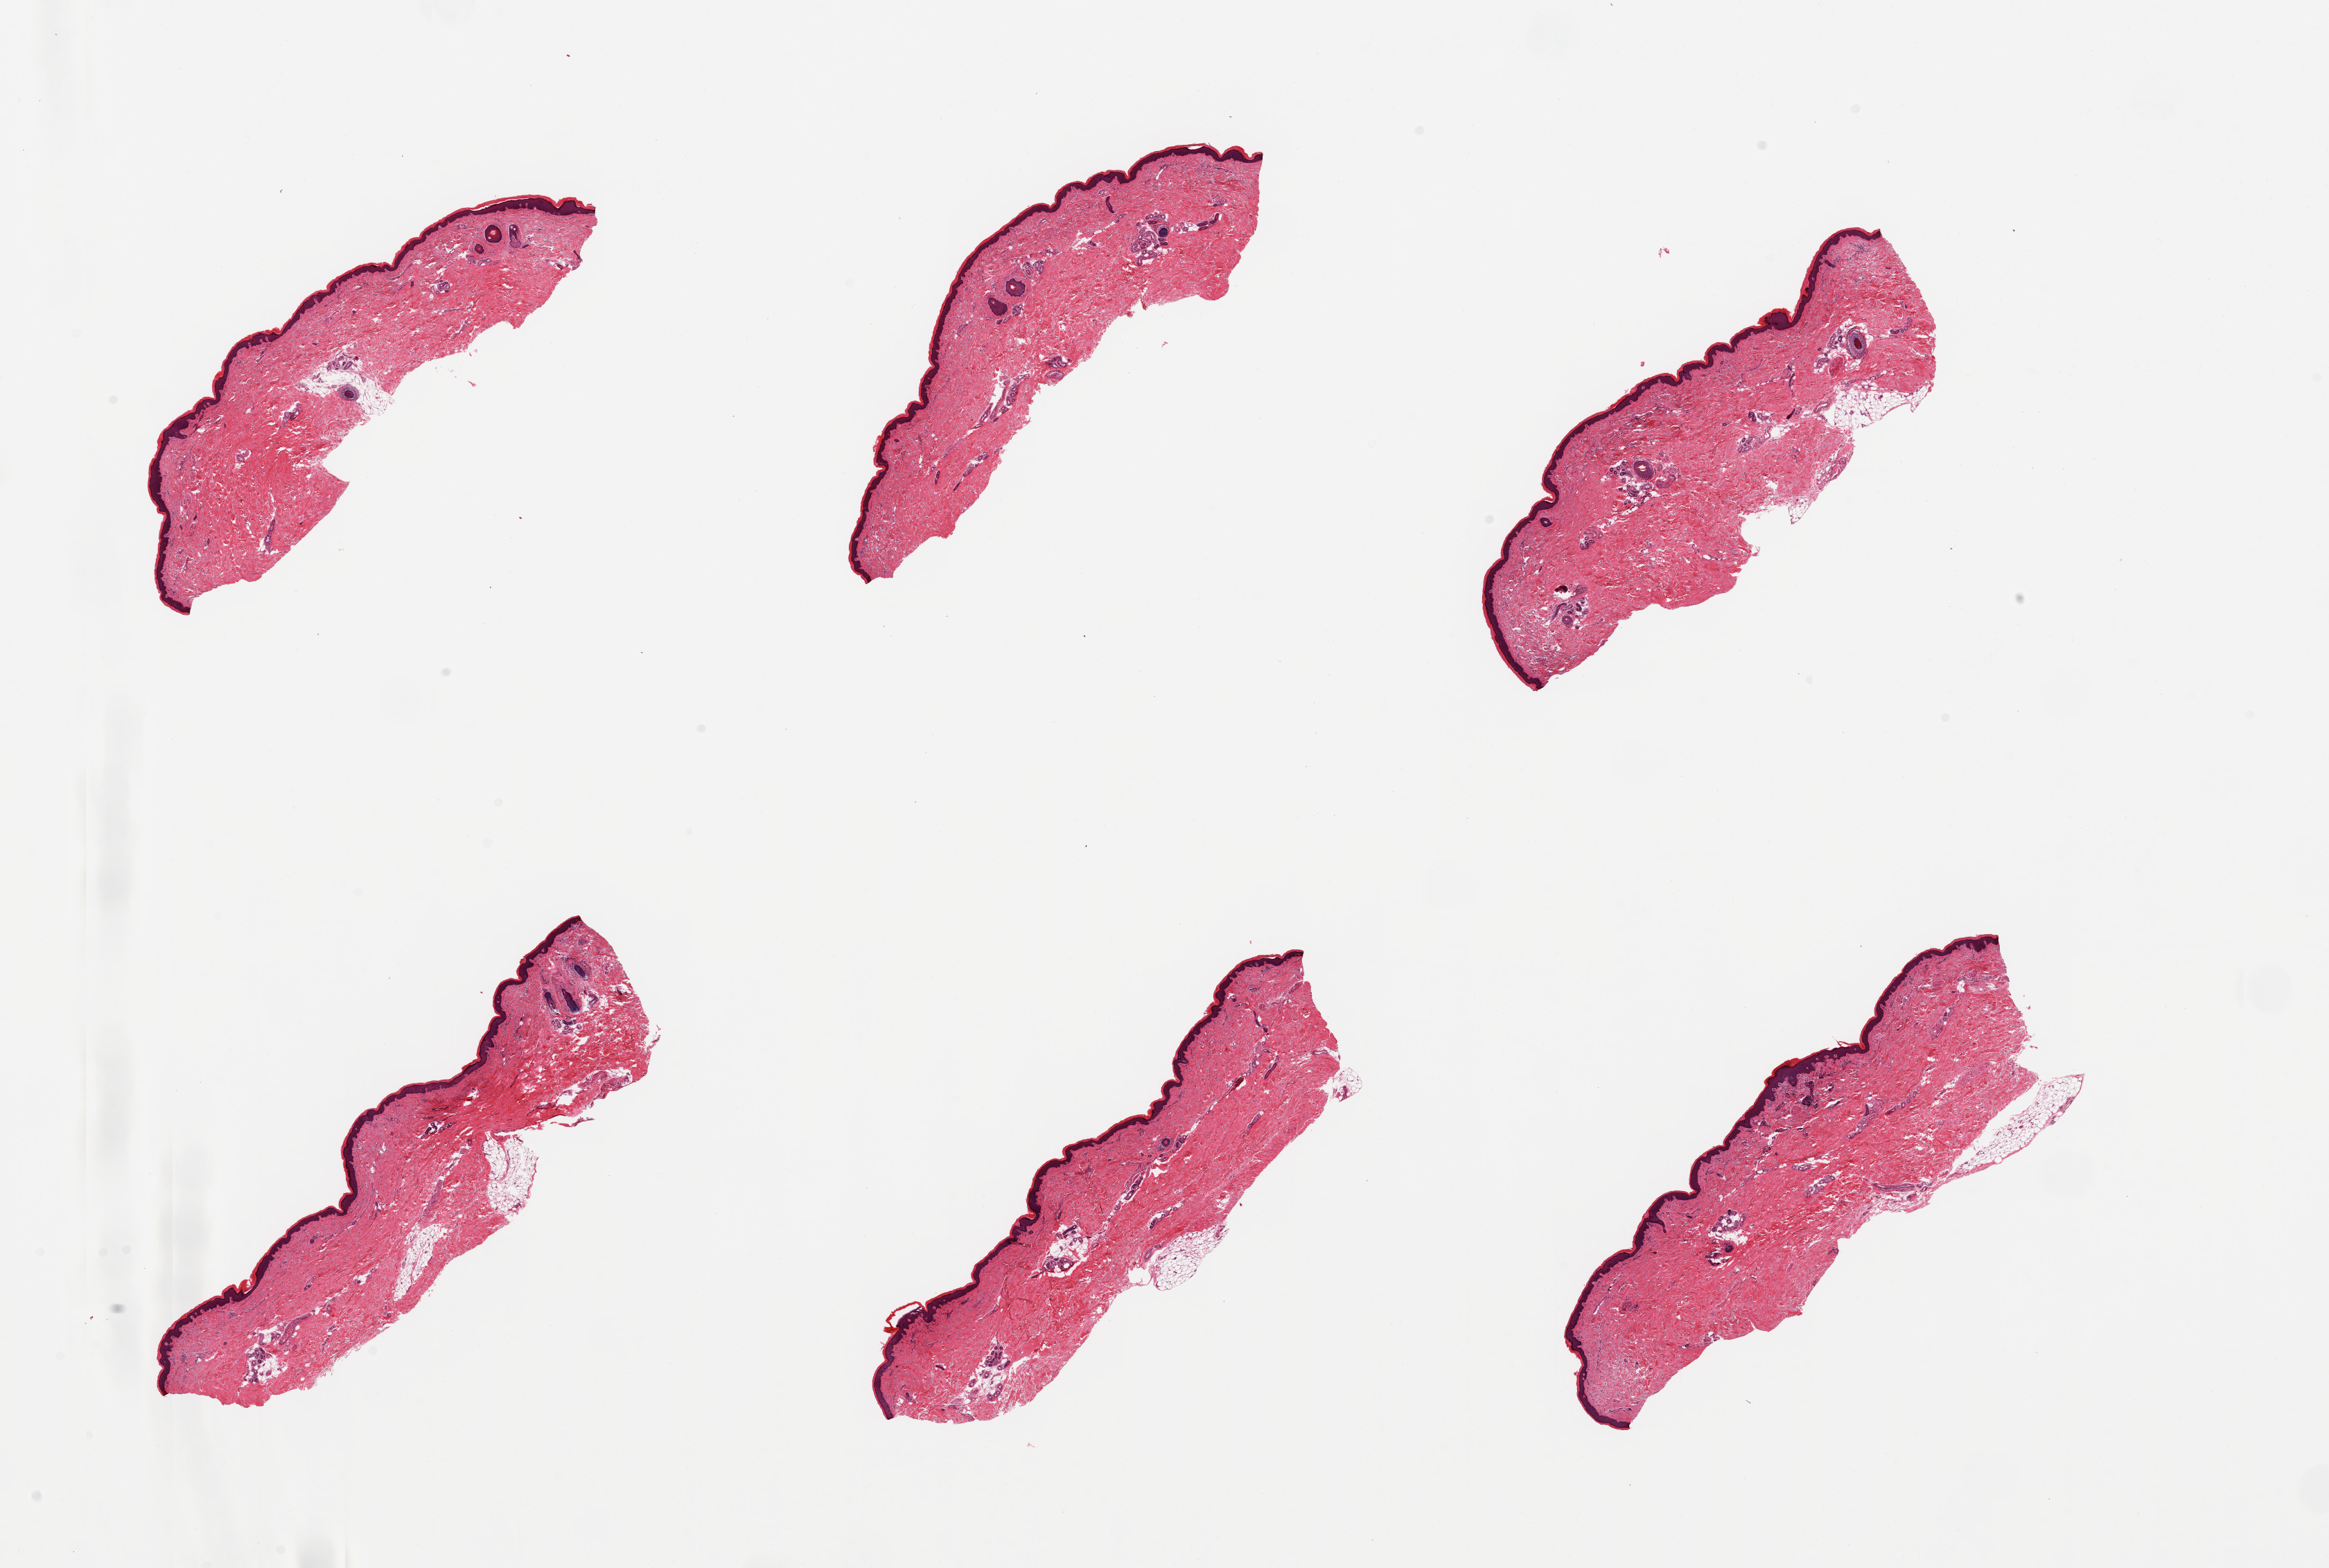
Whole-slide image, haematoxylin and eosin stain — shown as a low-resolution overview of the whole scanned area (about 26.6 x 17.9 mm); PAXgene-fixed, paraffin-embedded tissue; section of skin of lower leg (target tissue); tissue donor sample.
Reviewer comment on this tissue sample: 6 pieces; small amount of external/internal fat, epidermis is 49.3 um.